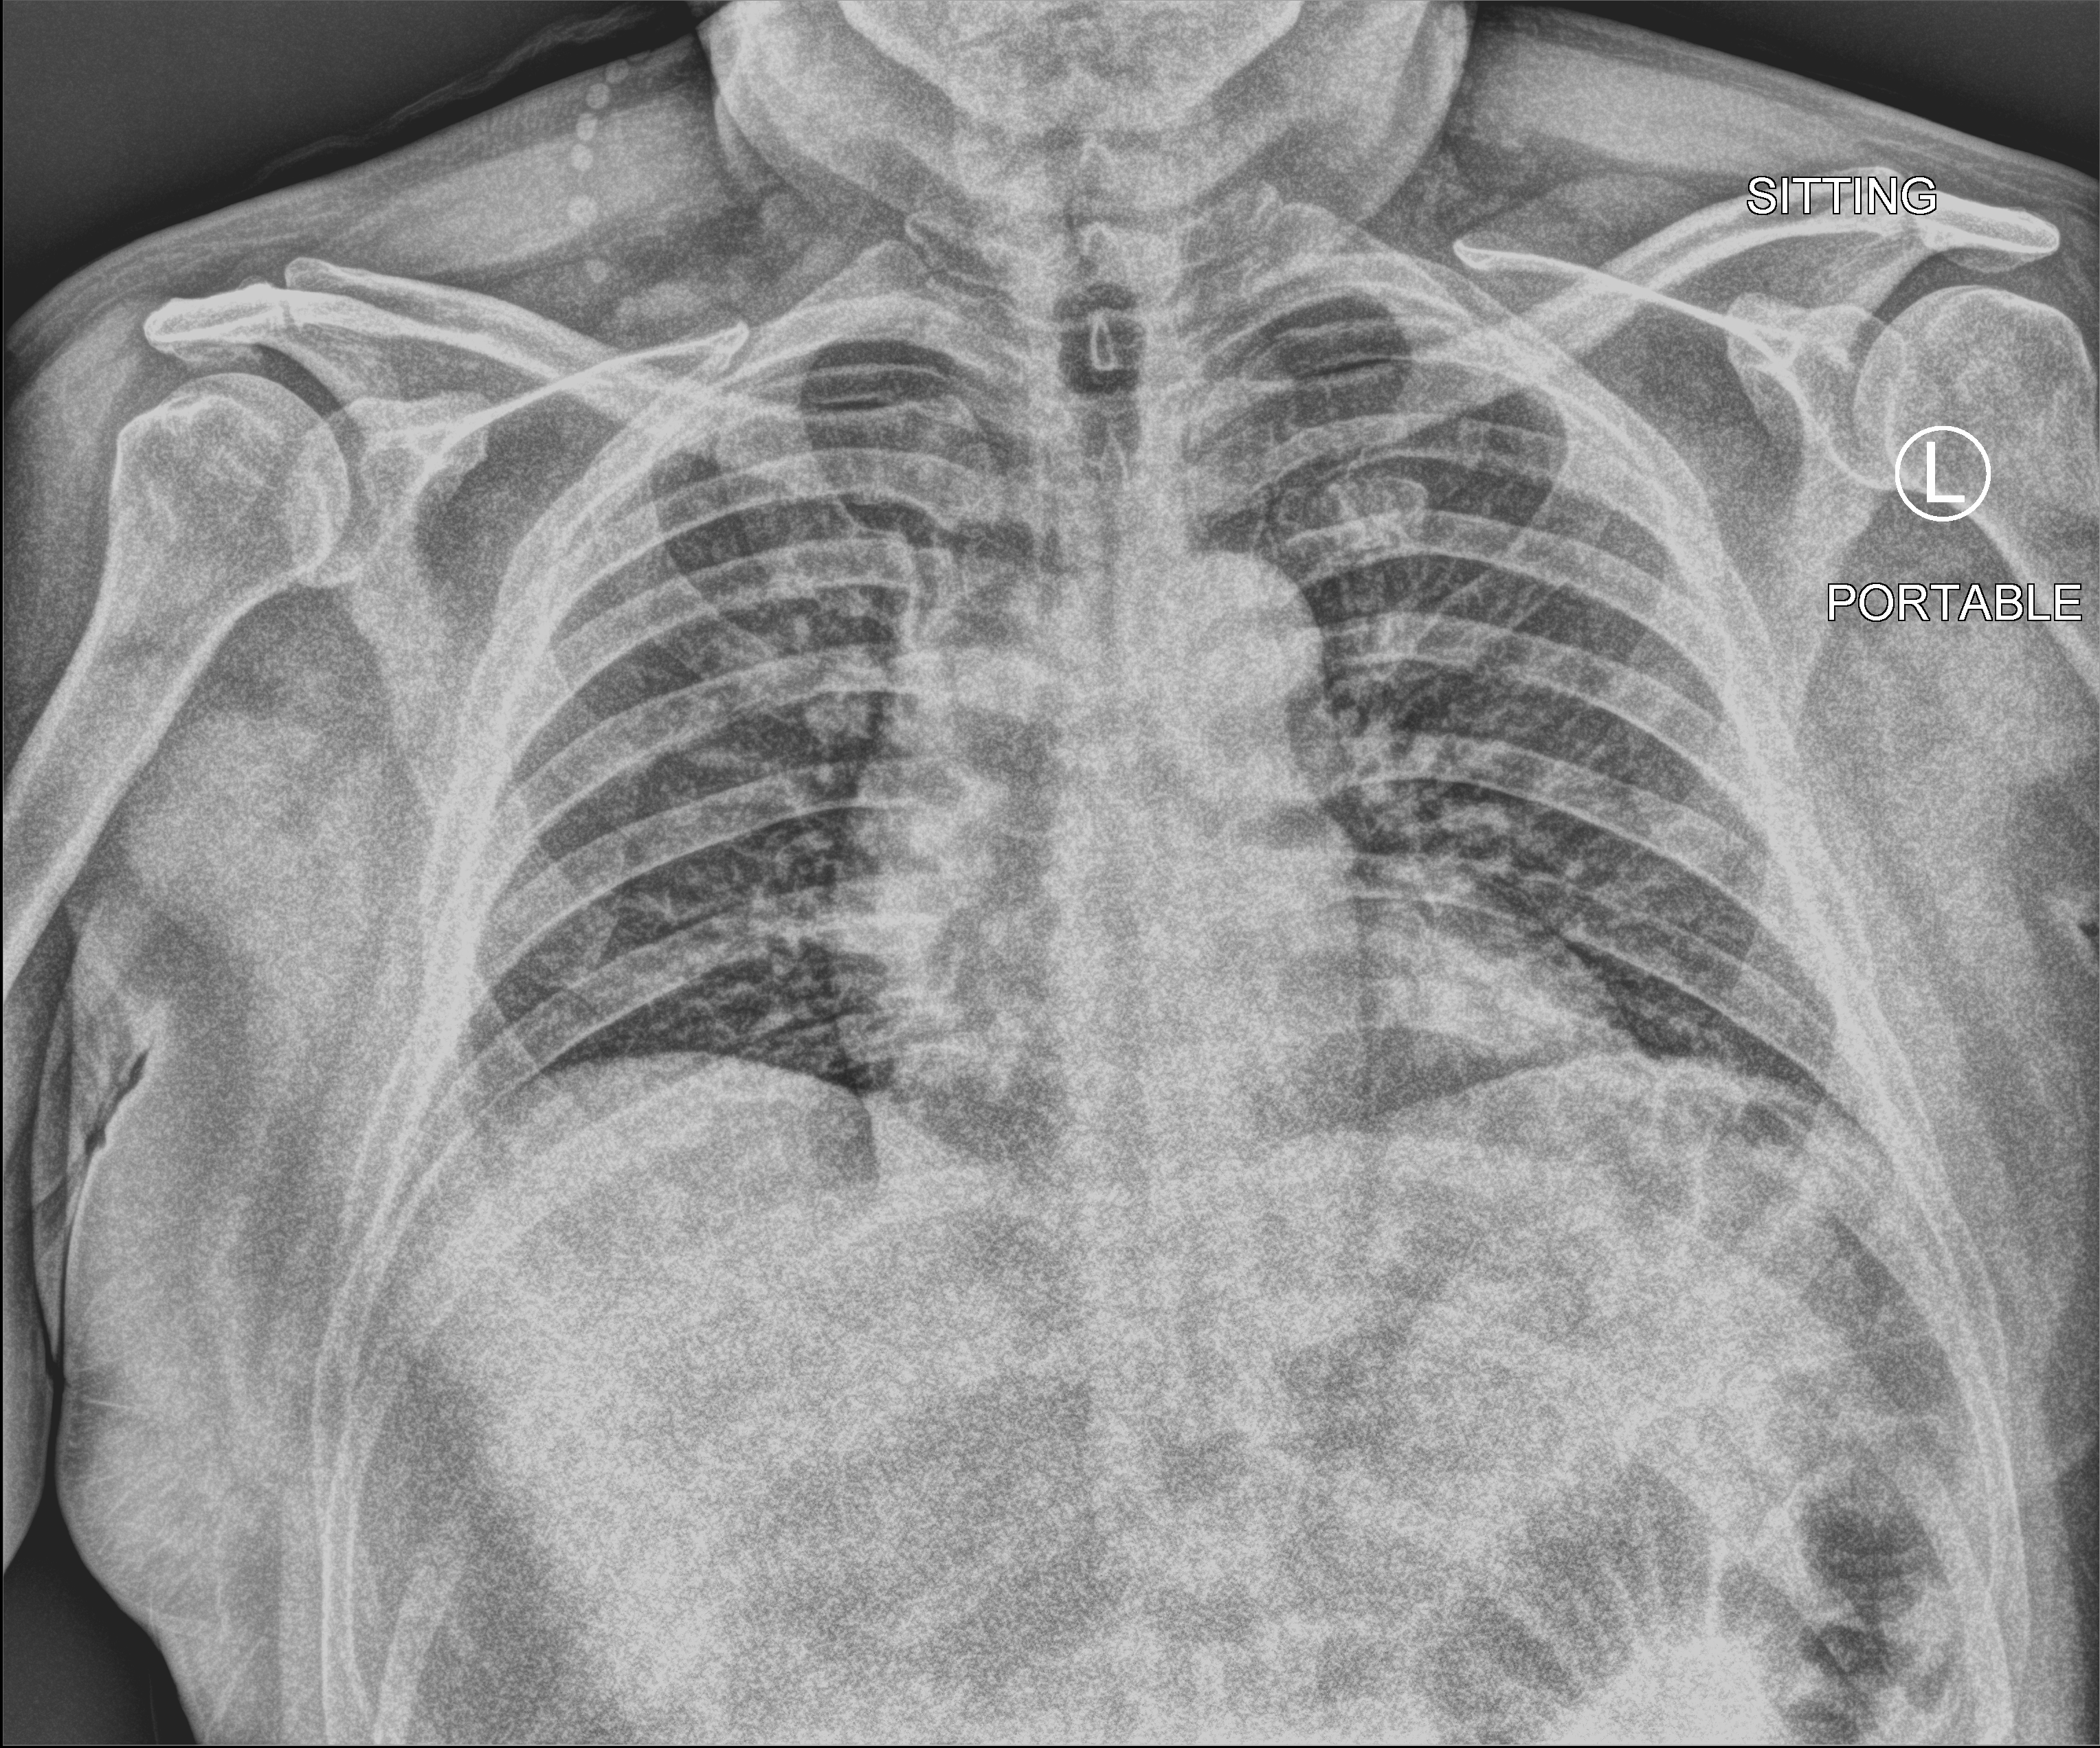
Chest X-ray (portable); anteroposterior (AP) projection. Patient hospitalised with COVID-19; male, aged 60–74 years.
From the hospital-stay record, not from the radiograph (when in the stay this image was taken is not recorded): admitted to intensive care during this hospital stay: no.